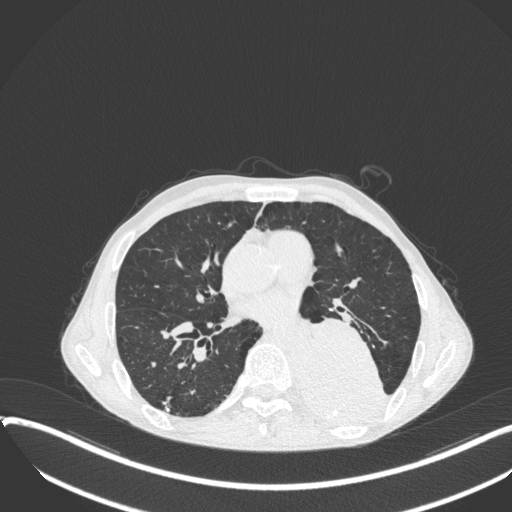
Chest CT, one axial slice; position 182 of 400 along the scan axis; reconstruction kernel B31f; 120 kVp; lung window (W 1500 / L -600 HU); 512 × 512 image matrix. Male patient, age 57 years. From the clinical record (not read from this slice): clinical TNM (as recorded): T4 N0 M0.
Structures marked on this image (rectangle marked by the reading radiologist):
- lung tumour (recorded histology: squamous cell carcinoma): bounding box [x1, y1, x2, y2] px = [294, 317, 392, 422]